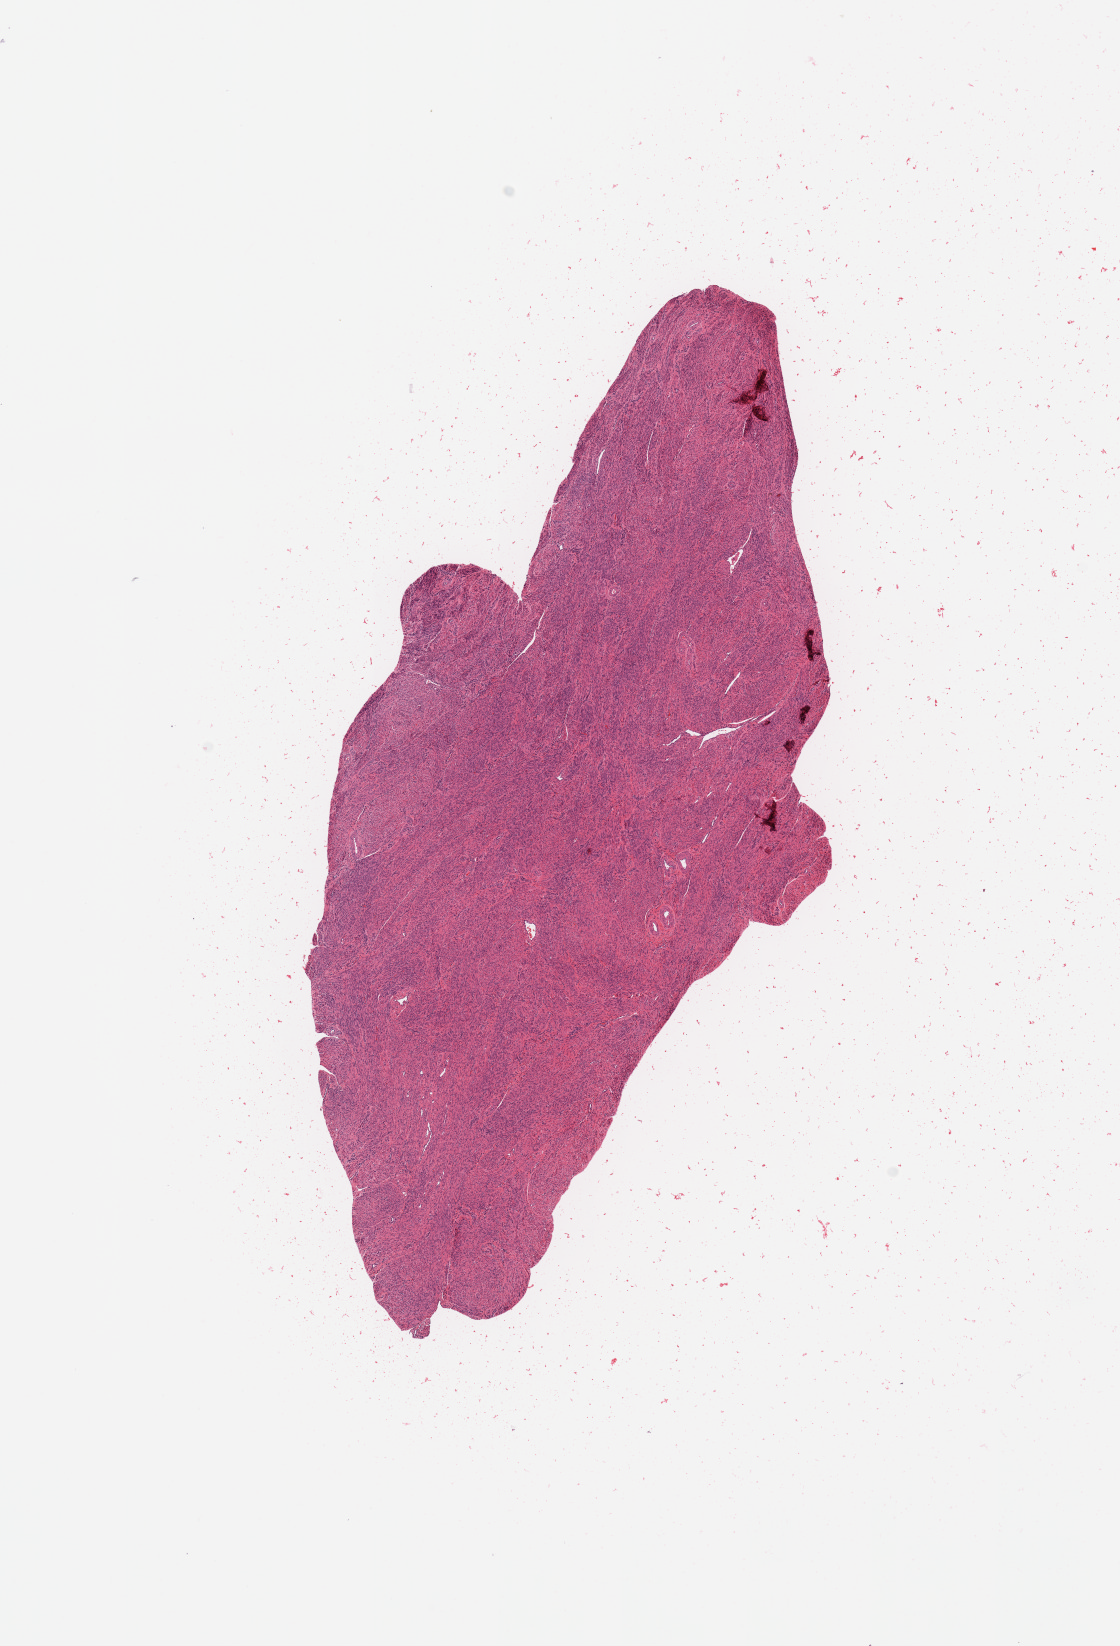
Digitized Hematoxylin and eosin (H&E) stained tissue section (whole slide) — whole scanned area (about 8.9 x 13.0 mm, slide scanned at 20x) shown as a low-resolution overview; normal (non-tumour) tissue sample, uterus. 42-year-old female patient.
This section: normal (non-tumour) tissue from the same patient. Patient diagnosis: Endometrioid adenocarcinoma, NOS.